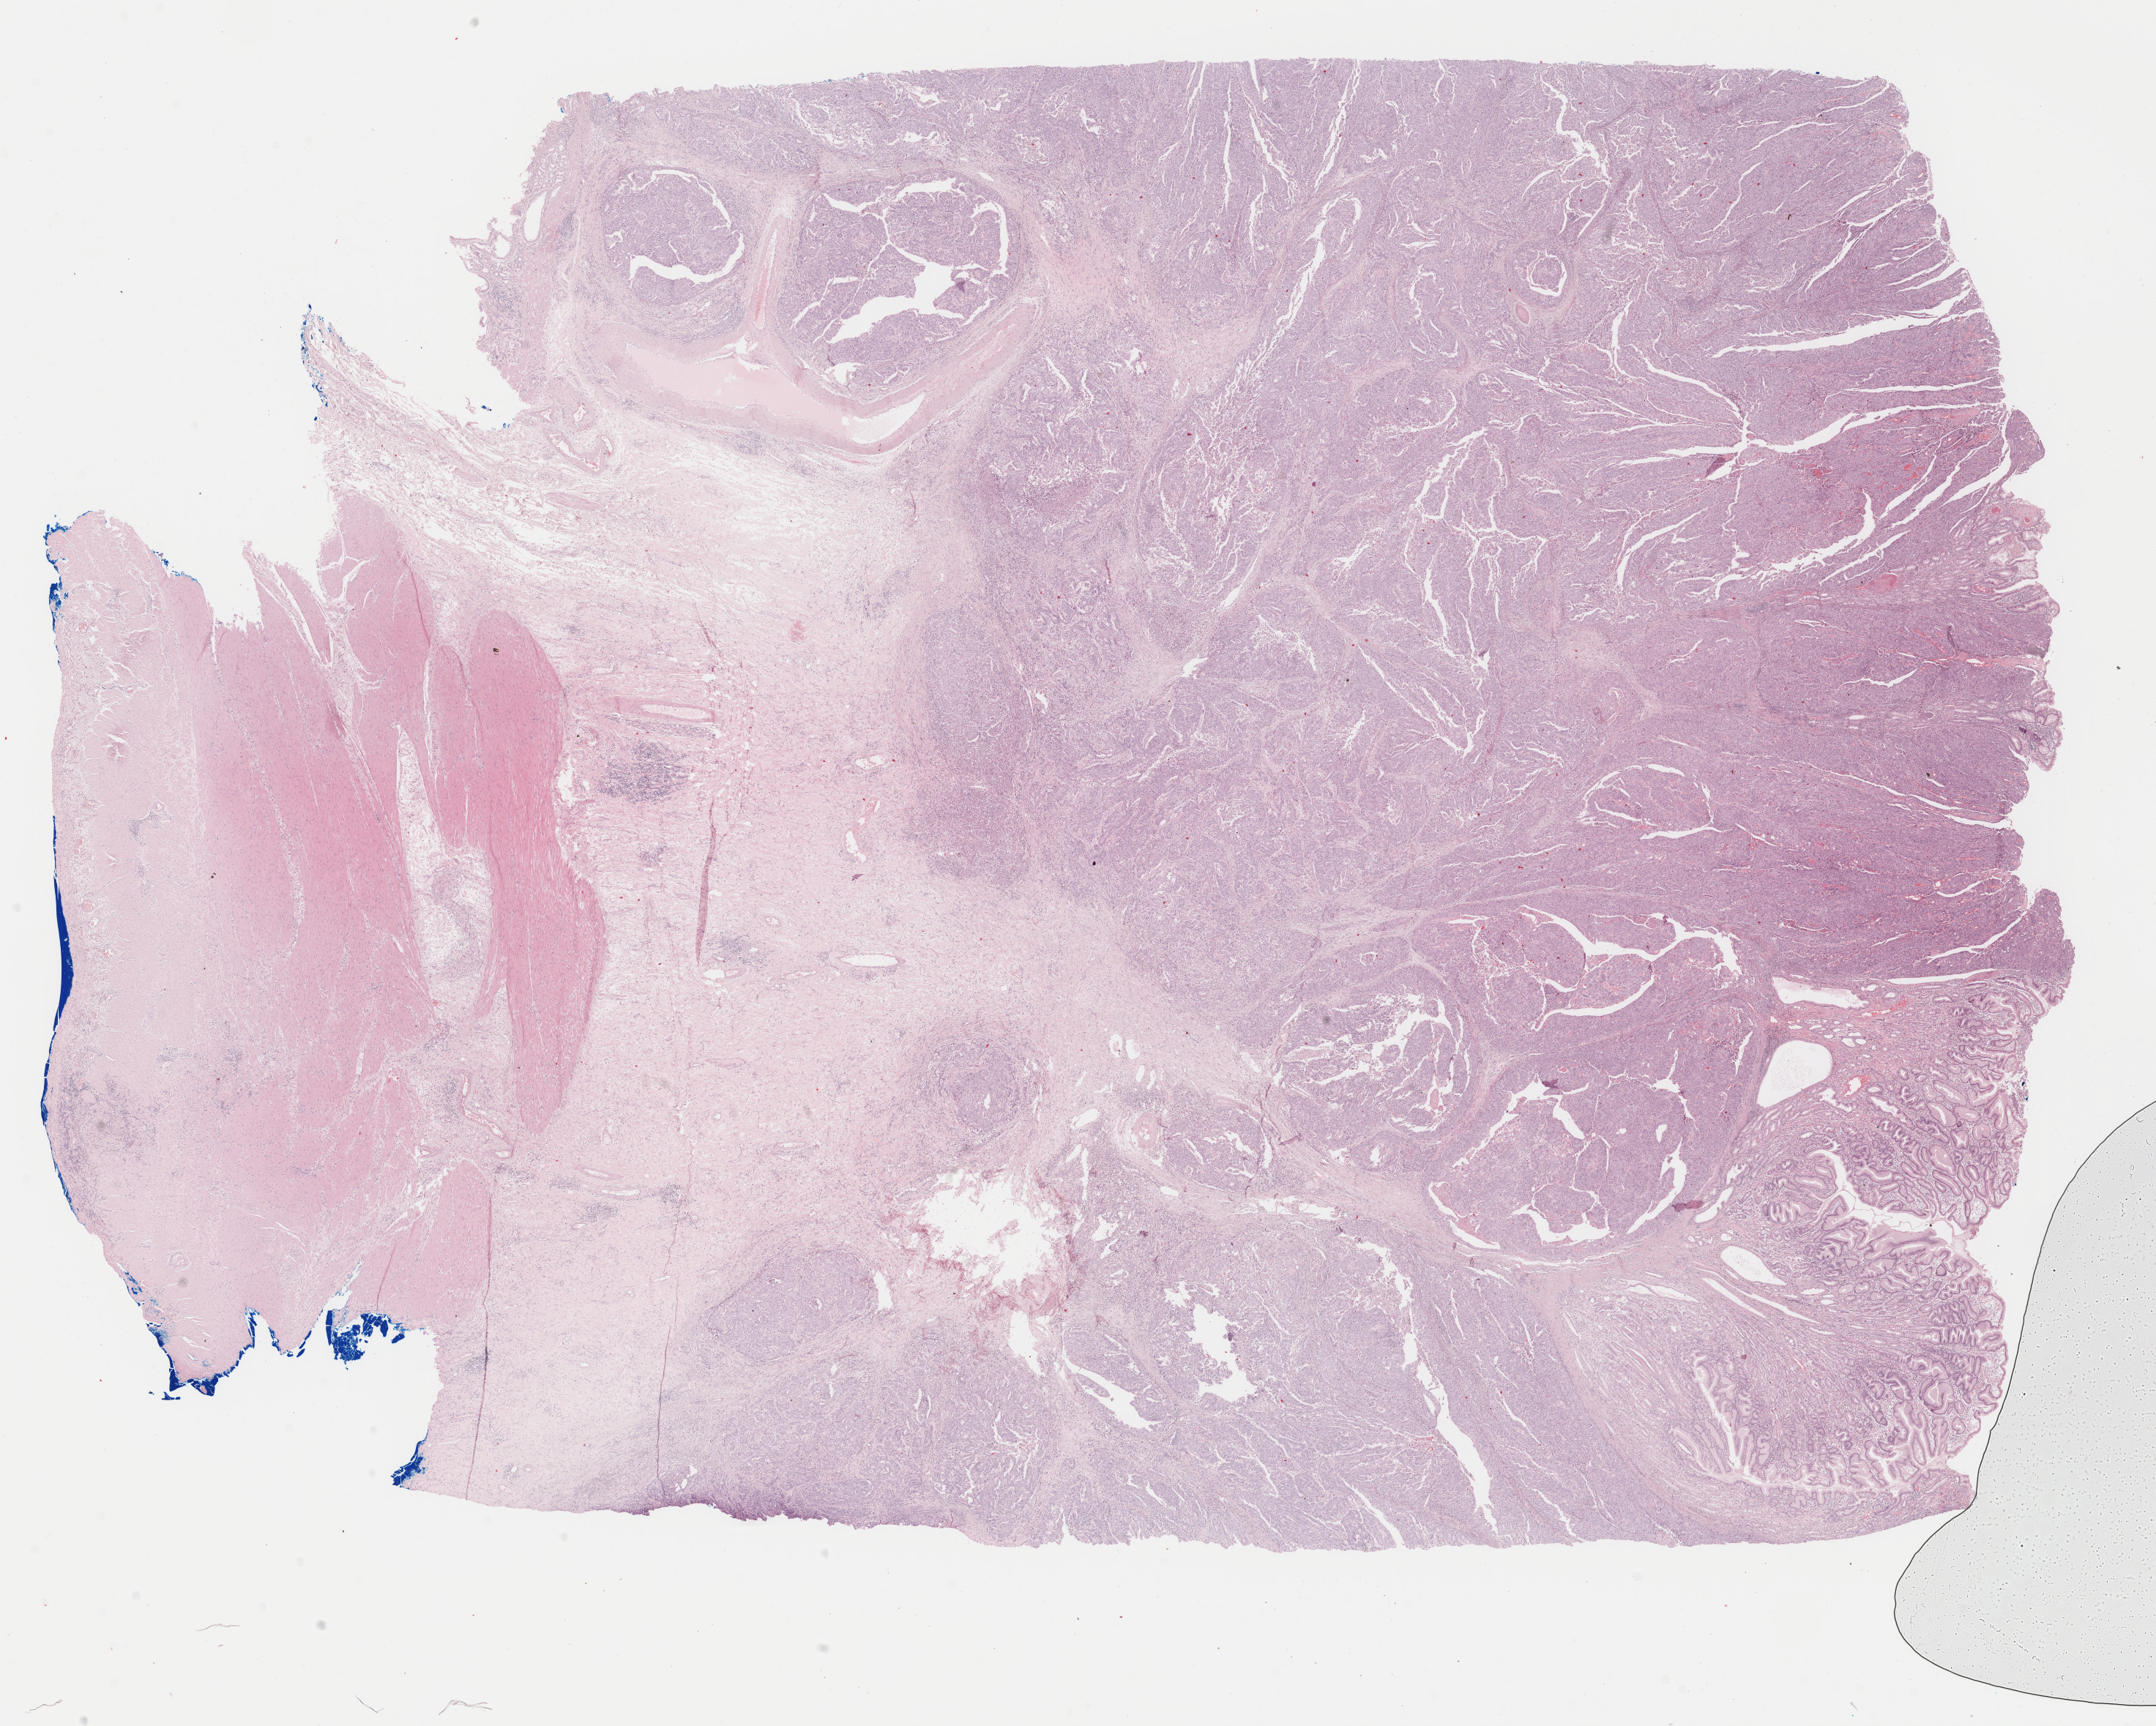
Digitized H&E-stained tissue section (whole slide), low-resolution overview of the scanned area, about 23.4 x 18.7 mm (slide scanned at 40x). Formalin-fixed paraffin-embedded (FFPE) diagnostic section. Sample: primary tumour, stomach. Male patient; age at initial diagnosis 57 years. Histologic grade: G3 (poorly differentiated).
Lymph nodes positive (case pathology): 0 of 20 examined. Histologic diagnosis: Tubular adenocarcinoma (fundus of stomach). AJCC pathologic stage: IIA.